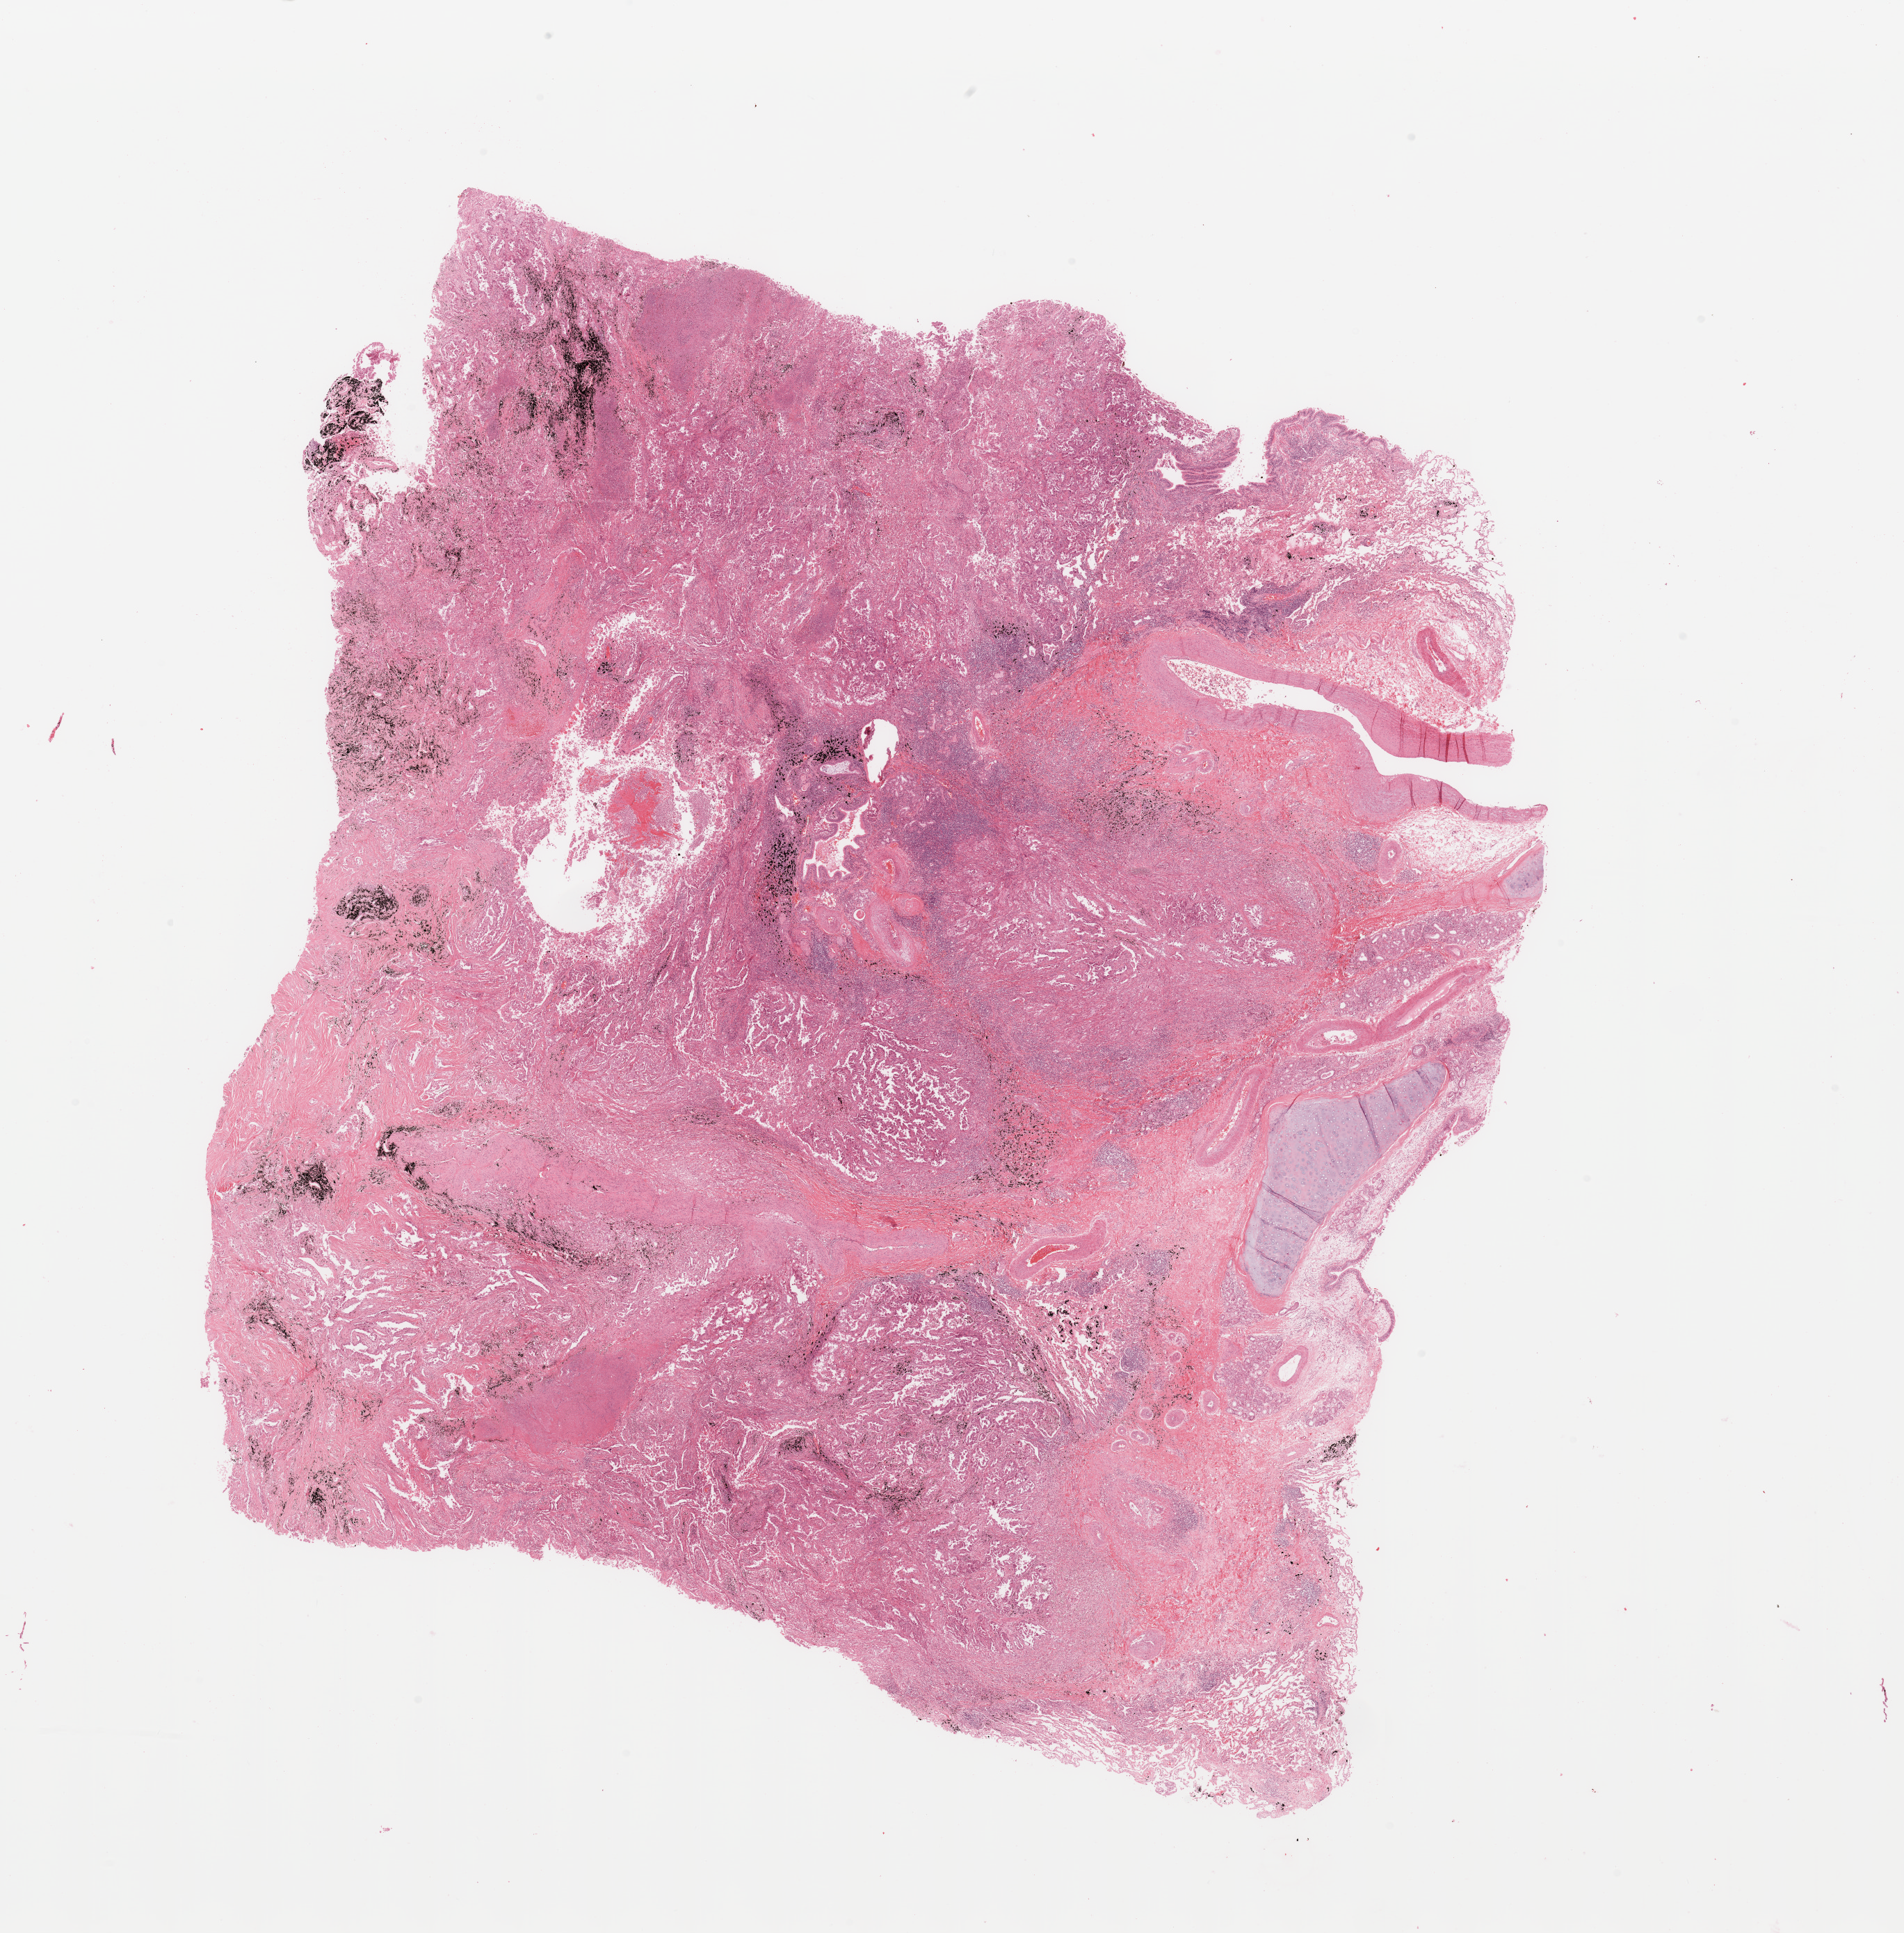
Digitized H&E-stained tissue section (whole slide) — a low-resolution overview of the entire scanned area, about 21.7 x 22.0 mm (slide scanned at 20x); tumour tissue sample, lung. Male, 65 y/o. Histologic grade: G3 (poorly differentiated).
- AJCC pathologic stage: IB
- histologic diagnosis: Adenocarcinoma, NOS